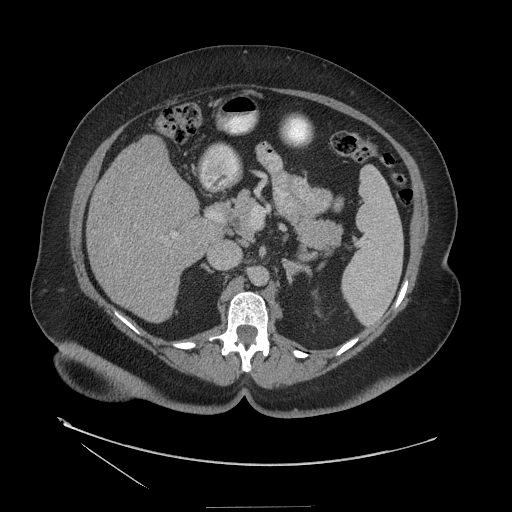
Contrast-enhanced abdominal CT (liver protocol), one axial slice; reconstruction kernel STANDARD; soft-tissue window (W 400 / L 40 HU); 512 × 512 image matrix. From the clinical record (not read from this slice): diagnosis: hepatocellular carcinoma (patient treated with transarterial chemoembolisation; whether this scan precedes or follows treatment is not stated here); TNM stage (as recorded): Stage-II; Child-Pugh class: A; tumour size: 3 cm.
Structures marked on this image (semi-automatic segmentation, software-assisted and operator-edited):
- liver parenchyma outside the tumour (the mass and vessels are separate outlines, so this box may not span the whole liver): bounding box (x1, y1, x2, y2) in pixels: (86, 136, 216, 322)